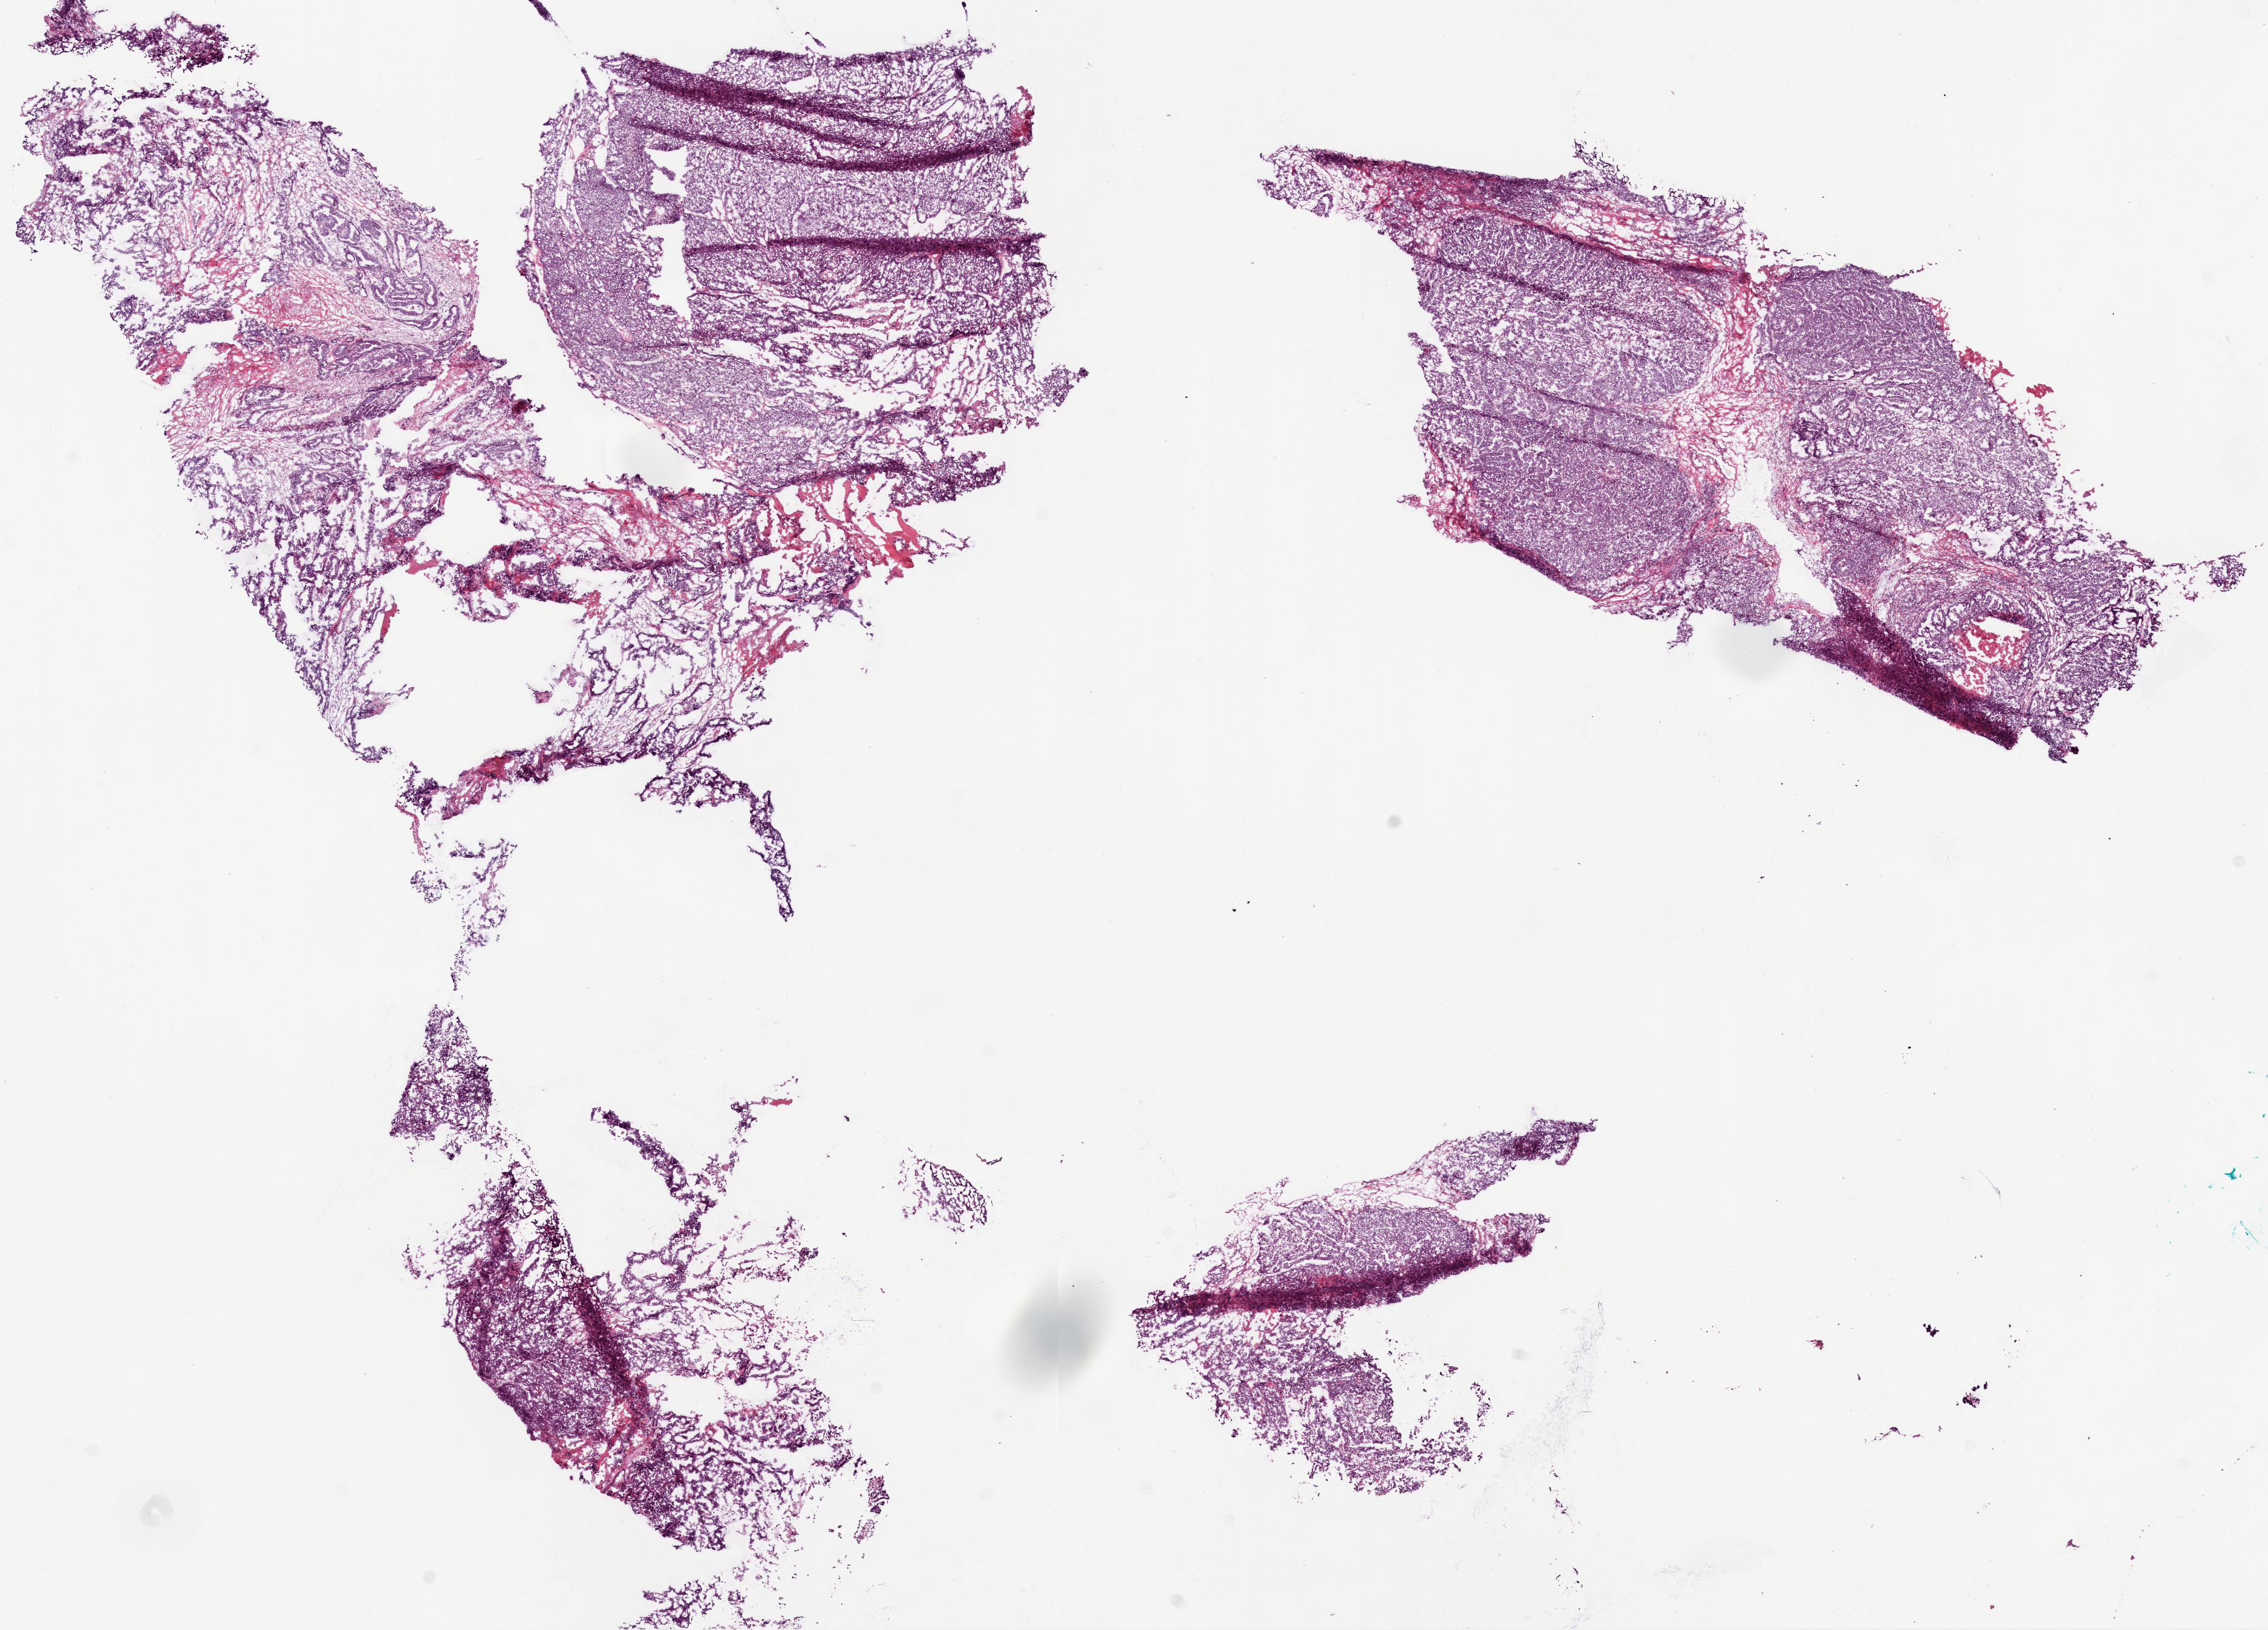
Digitized Hematoxylin and eosin (H&E) stained tissue section (whole slide), low-resolution overview of the scanned area, about 15.0 x 10.8 mm; frozen section from the bottom of the tissue portion; ovary, primary tumour sample. Female patient; age at initial diagnosis 71 years. Histologic grade: G3 (poorly differentiated). Pathologist review of this section (percent, as recorded): tumour cells 95%, tumour nuclei 95%, normal cells 0%, stromal cells 4%, necrosis 1%.
- laterality: right
- diagnosis: Serous cystadenocarcinoma, NOS
- FIGO stage: IIIC